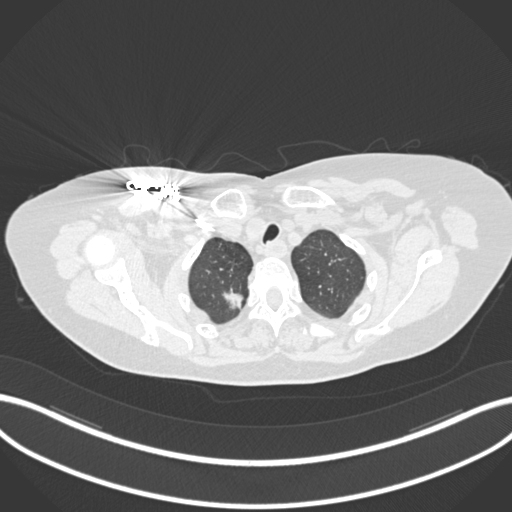
Chest CT, one axial slice; position 158 of 176 along the scan axis; reconstruction kernel B30f; 120 kVp; lung window (W 1500 / L -600 HU); 1 mm slice thickness; 512 × 512 image matrix. Patient: female, 72 years. From the clinical record (not read from this slice): clinical TNM (as recorded): T1c N0 M0.
Annotated regions visible in this slice (rectangle marked by the reading radiologist):
- lung tumour (recorded histology: adenocarcinoma): bounding box (x1, y1, x2, y2) in pixels: (218, 285, 244, 313)